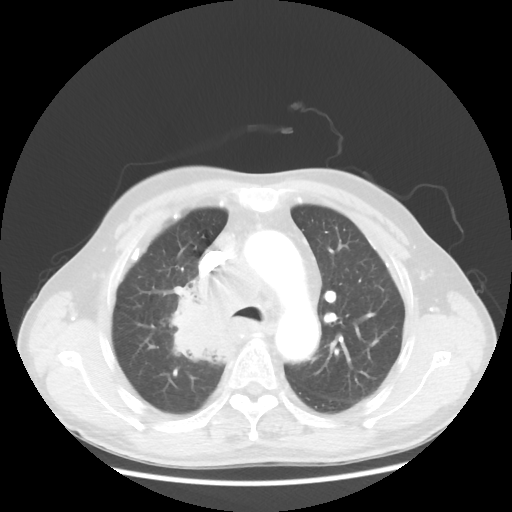
Chest CT, one axial slice; position 87 of 124 along the scan axis; reconstruction kernel STANDARD; lung window (W 1500 / L -600 HU); 5 mm slice thickness; 512 × 512 image matrix, field of view 382 × 382 mm. Male patient, age 64 years. From the clinical record (not read from this slice): clinical TNM (as recorded): T3 N3 M0.
Outlined on this slice (bounding box drawn by a radiologist):
- lung tumour (recorded histology: small cell carcinoma): bounding box <158,277,243,383> (left, top, right, bottom; pixels)